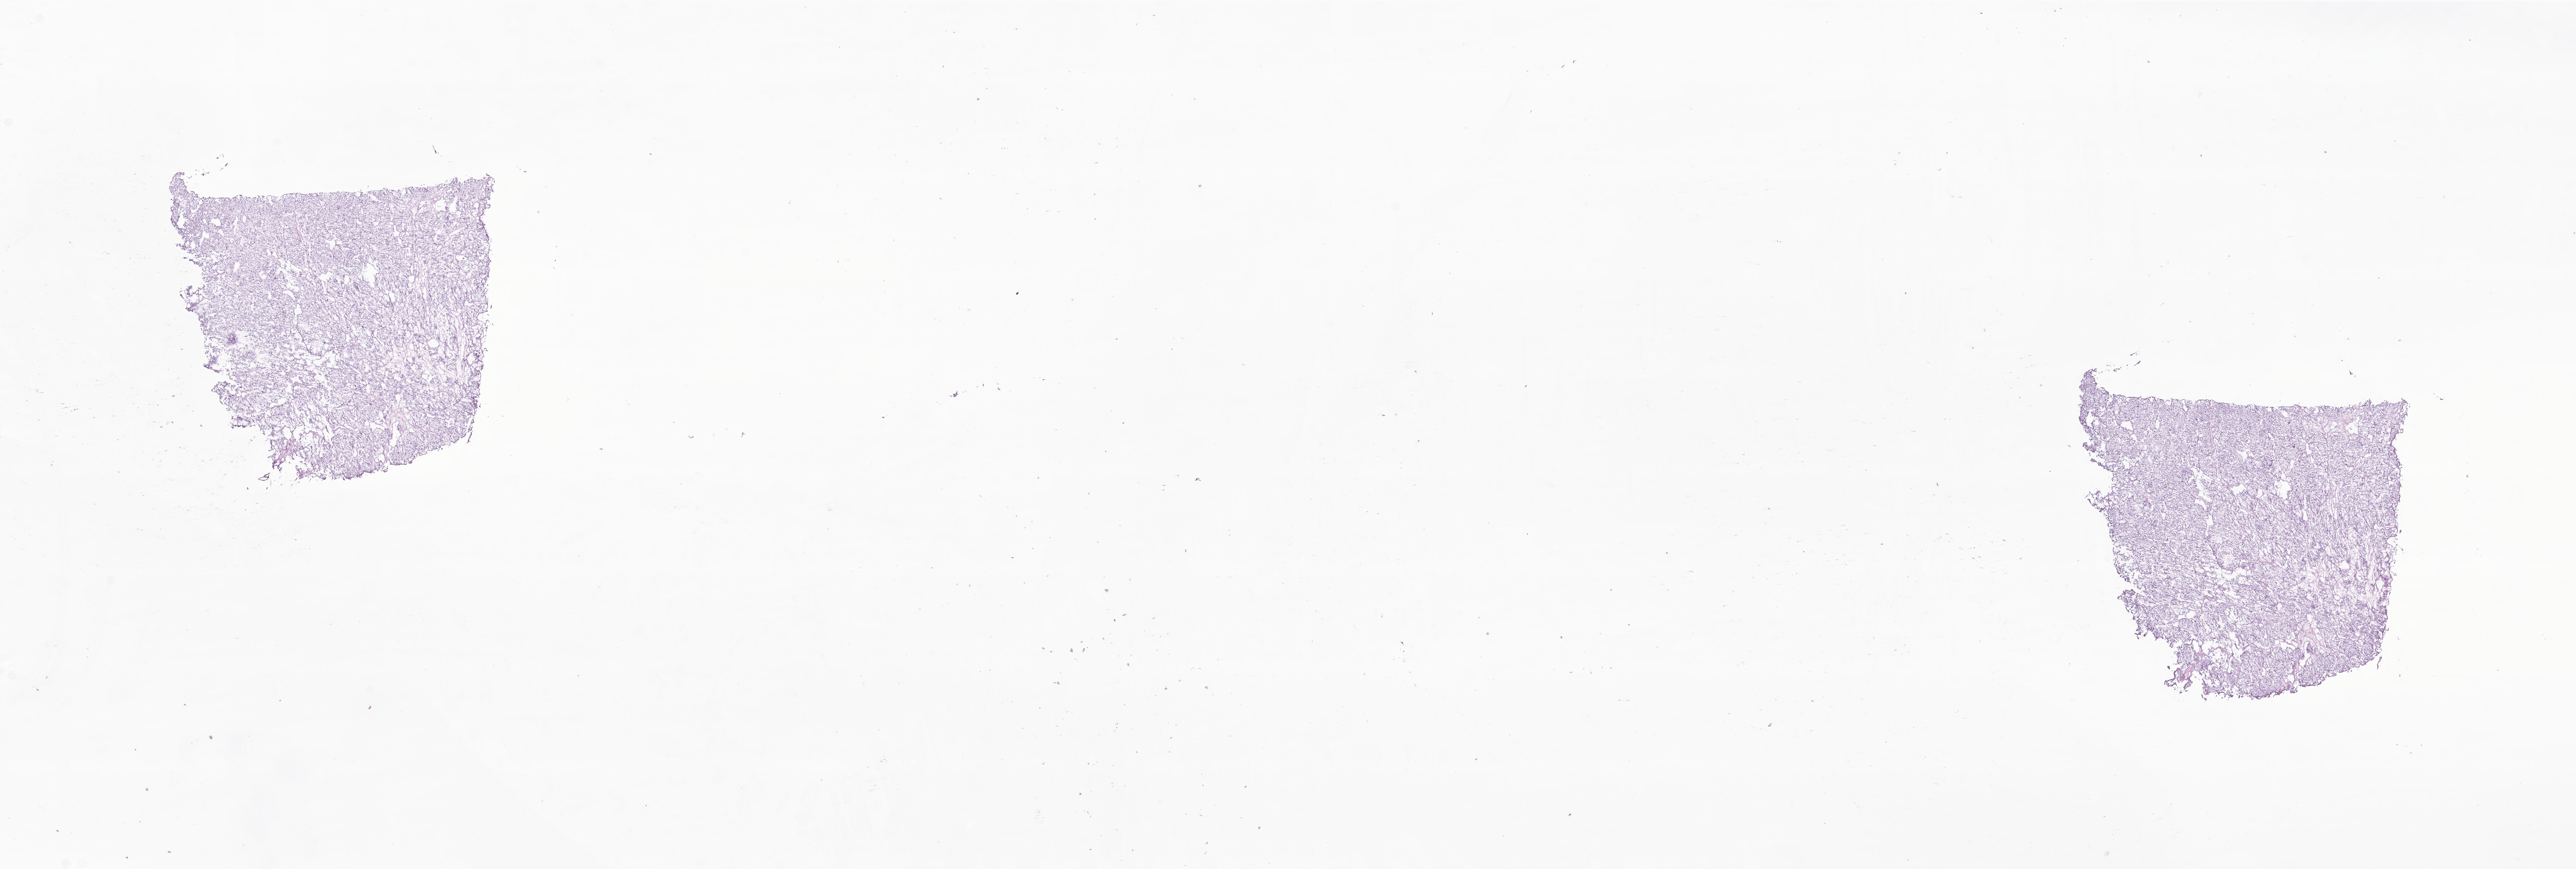
Digitized H&E-stained section of tumor tissue from the adrenal gland — whole scanned area (about 27.9 x 9.4 mm) shown as a low-resolution overview. Male patient, age 139 months.
Specimen: frozen section.